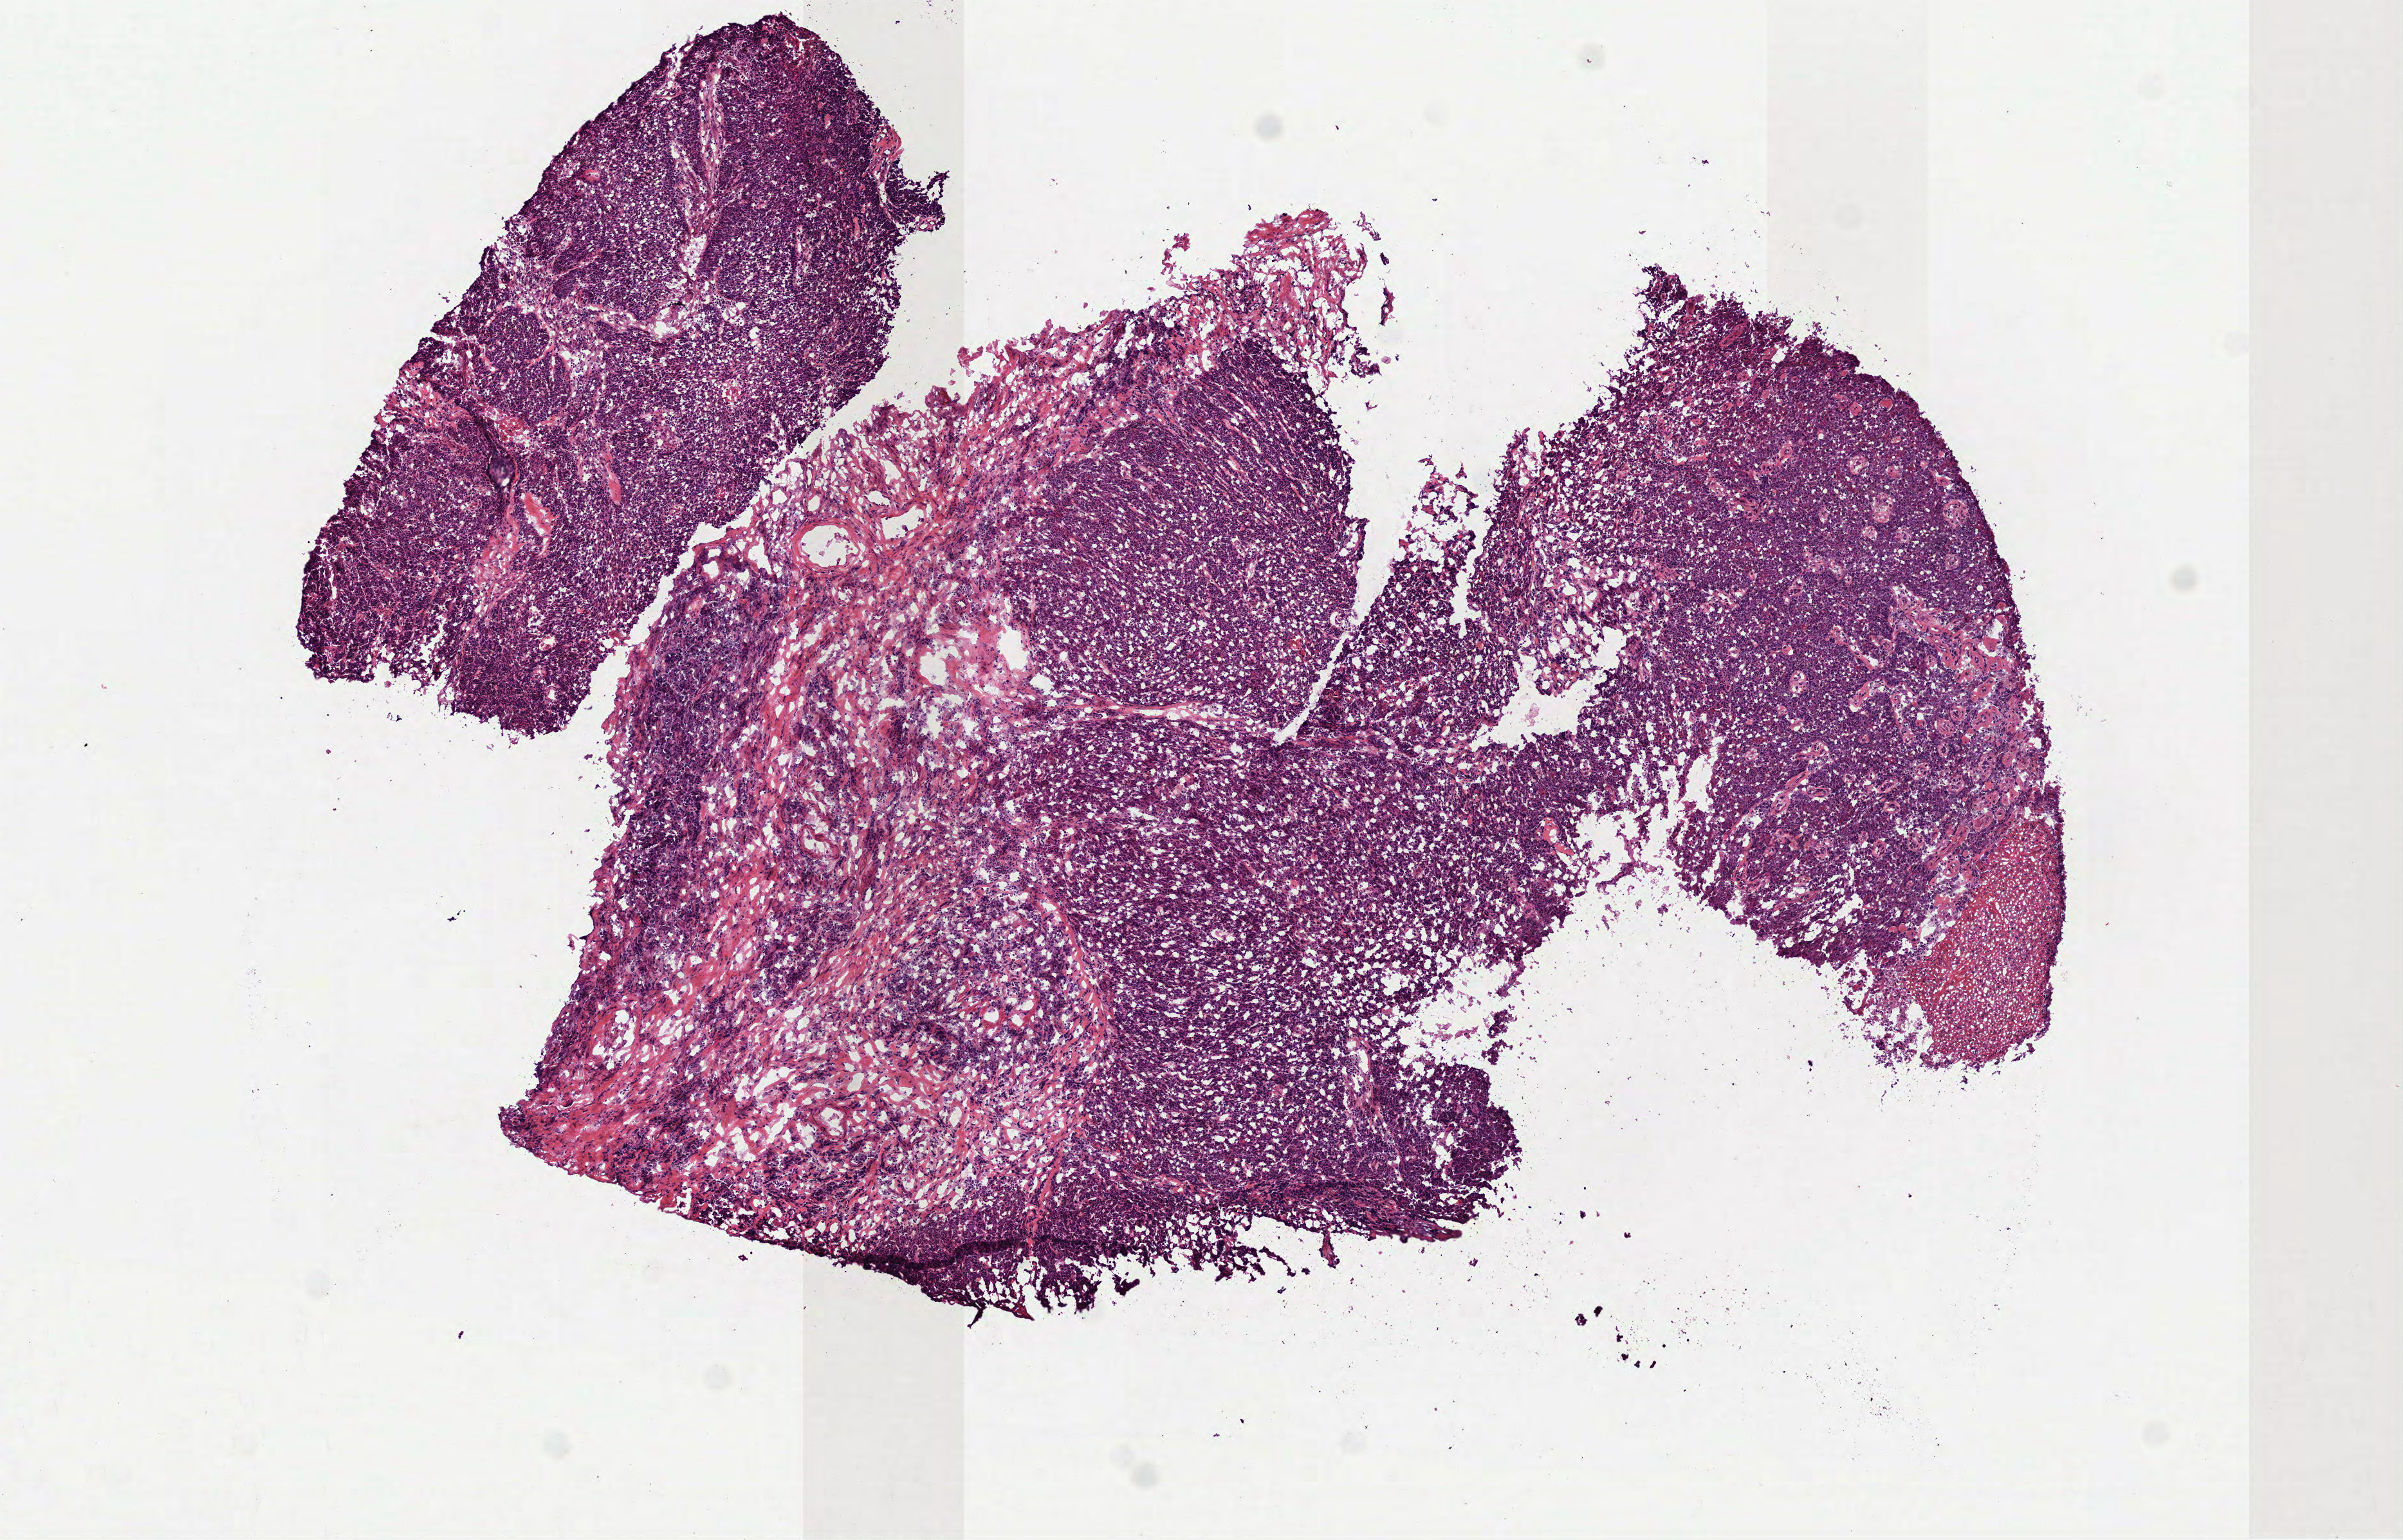
Digitized H&E-stained tissue section (whole slide), low-resolution overview of the scanned area, about 7.5 x 4.8 mm; frozen section from the top of the tissue portion; sample: primary tumour, head and neck. Male patient; age at initial diagnosis 57 years. Histologic grade: G3 (poorly differentiated). Slide review estimates, as recorded: tumour cells 80%, tumour nuclei 70%, normal cells 0%, stromal cells 20%, necrosis 0%. Infiltration values recorded for this section: lymphocyte infiltration 25%, monocyte infiltration 0%, neutrophil infiltration 0%.
• AJCC pathologic stage: II (7th edition)
• pathologic diagnosis: Squamous cell carcinoma, NOS (tongue, NOS)